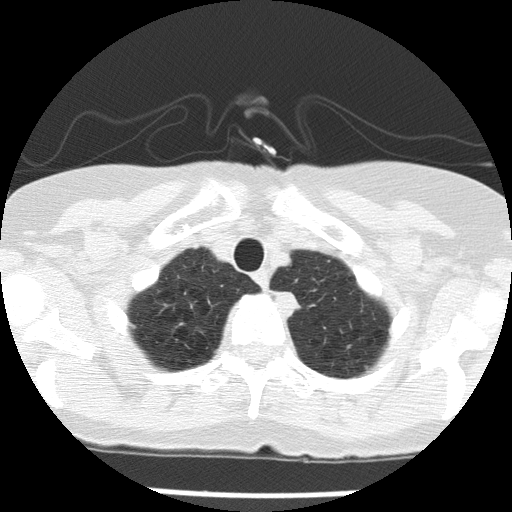
Low-dose screening chest CT, one axial slice. Slice 128 of 143 in the series (ordered by position). Reconstruction kernel FC51. 120 kVp. Lung window (W 1500 / L -600 HU). 2 mm slice thickness. 512 × 512 image matrix.
Structures marked on this image (outlined manually by an expert reader):
- lesion 1 (tumor, upper lobe of left lung): box from (x=274, y=291) to (x=301, y=319) px